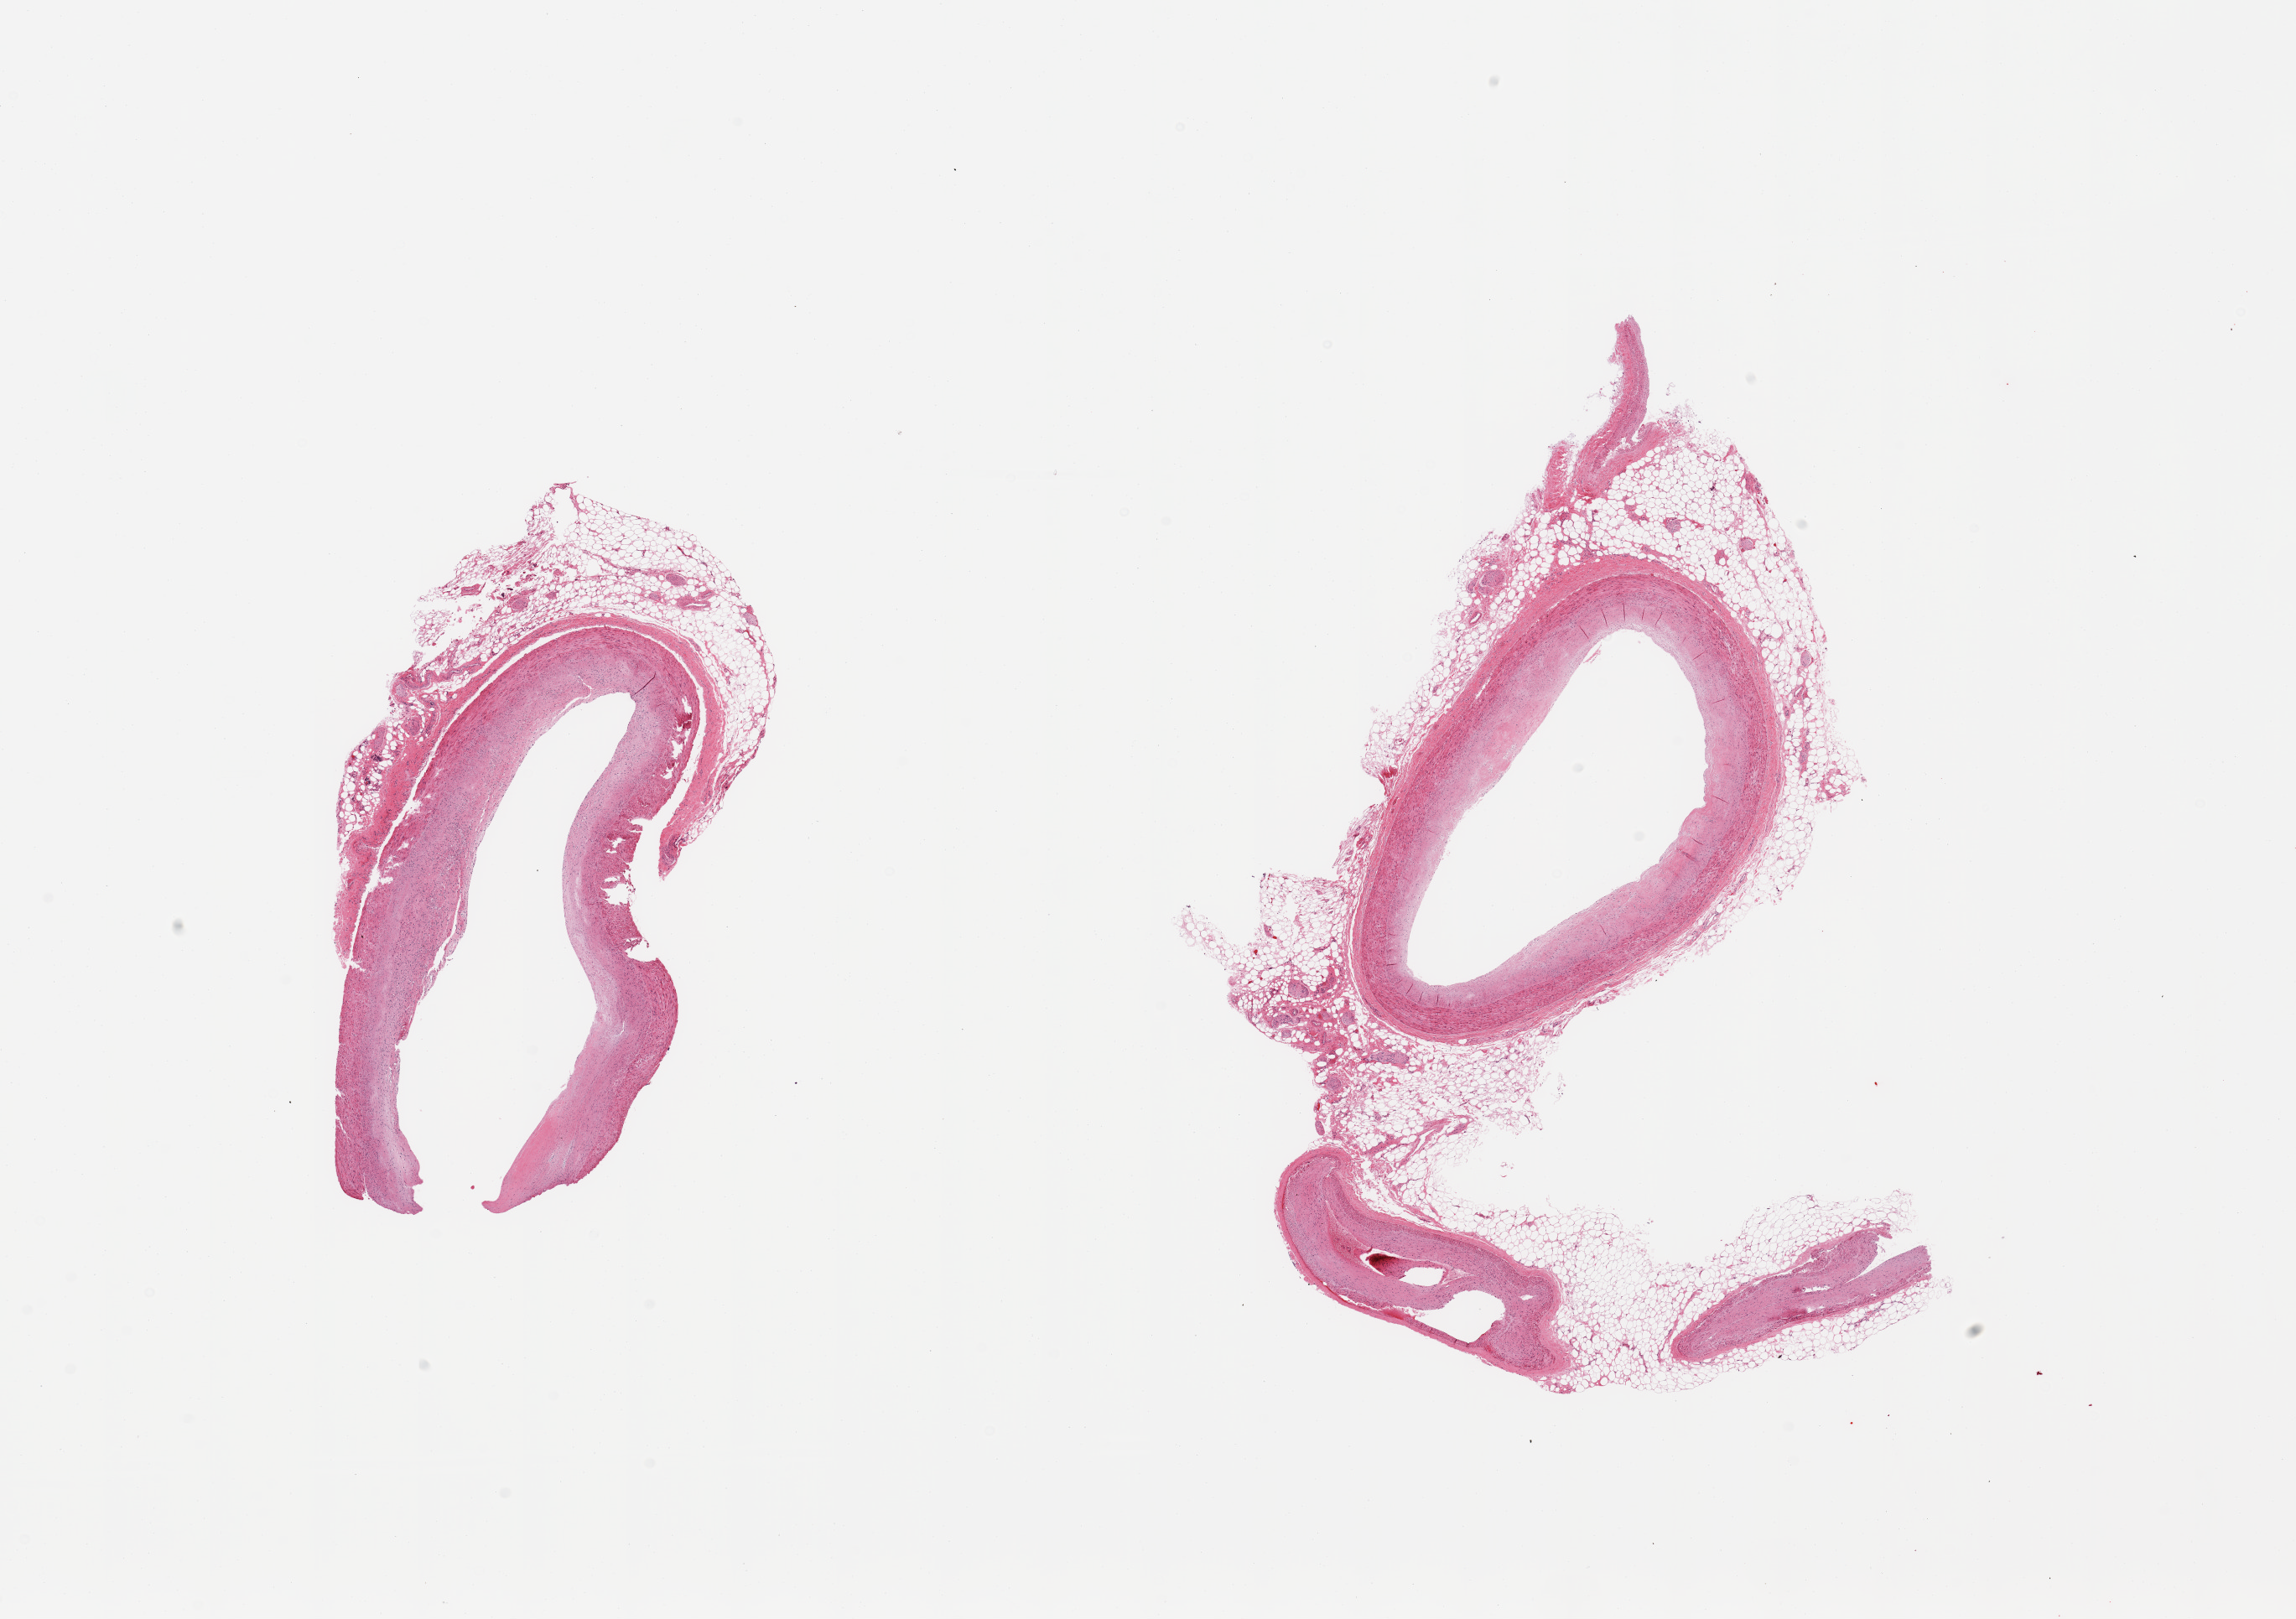
H&E whole-slide image, brightfield — low-resolution overview of the scanned area, about 21.7 x 15.3 mm, PAXgene-fixed, paraffin-embedded tissue, target tissue: coronary artery, tissue donor sample. Donor: male.
- review note (as recorded): 6 pieces; flat fibrous intimal thickening up to 0.4mm; untrimmed perivascular fat up to 1mm thick